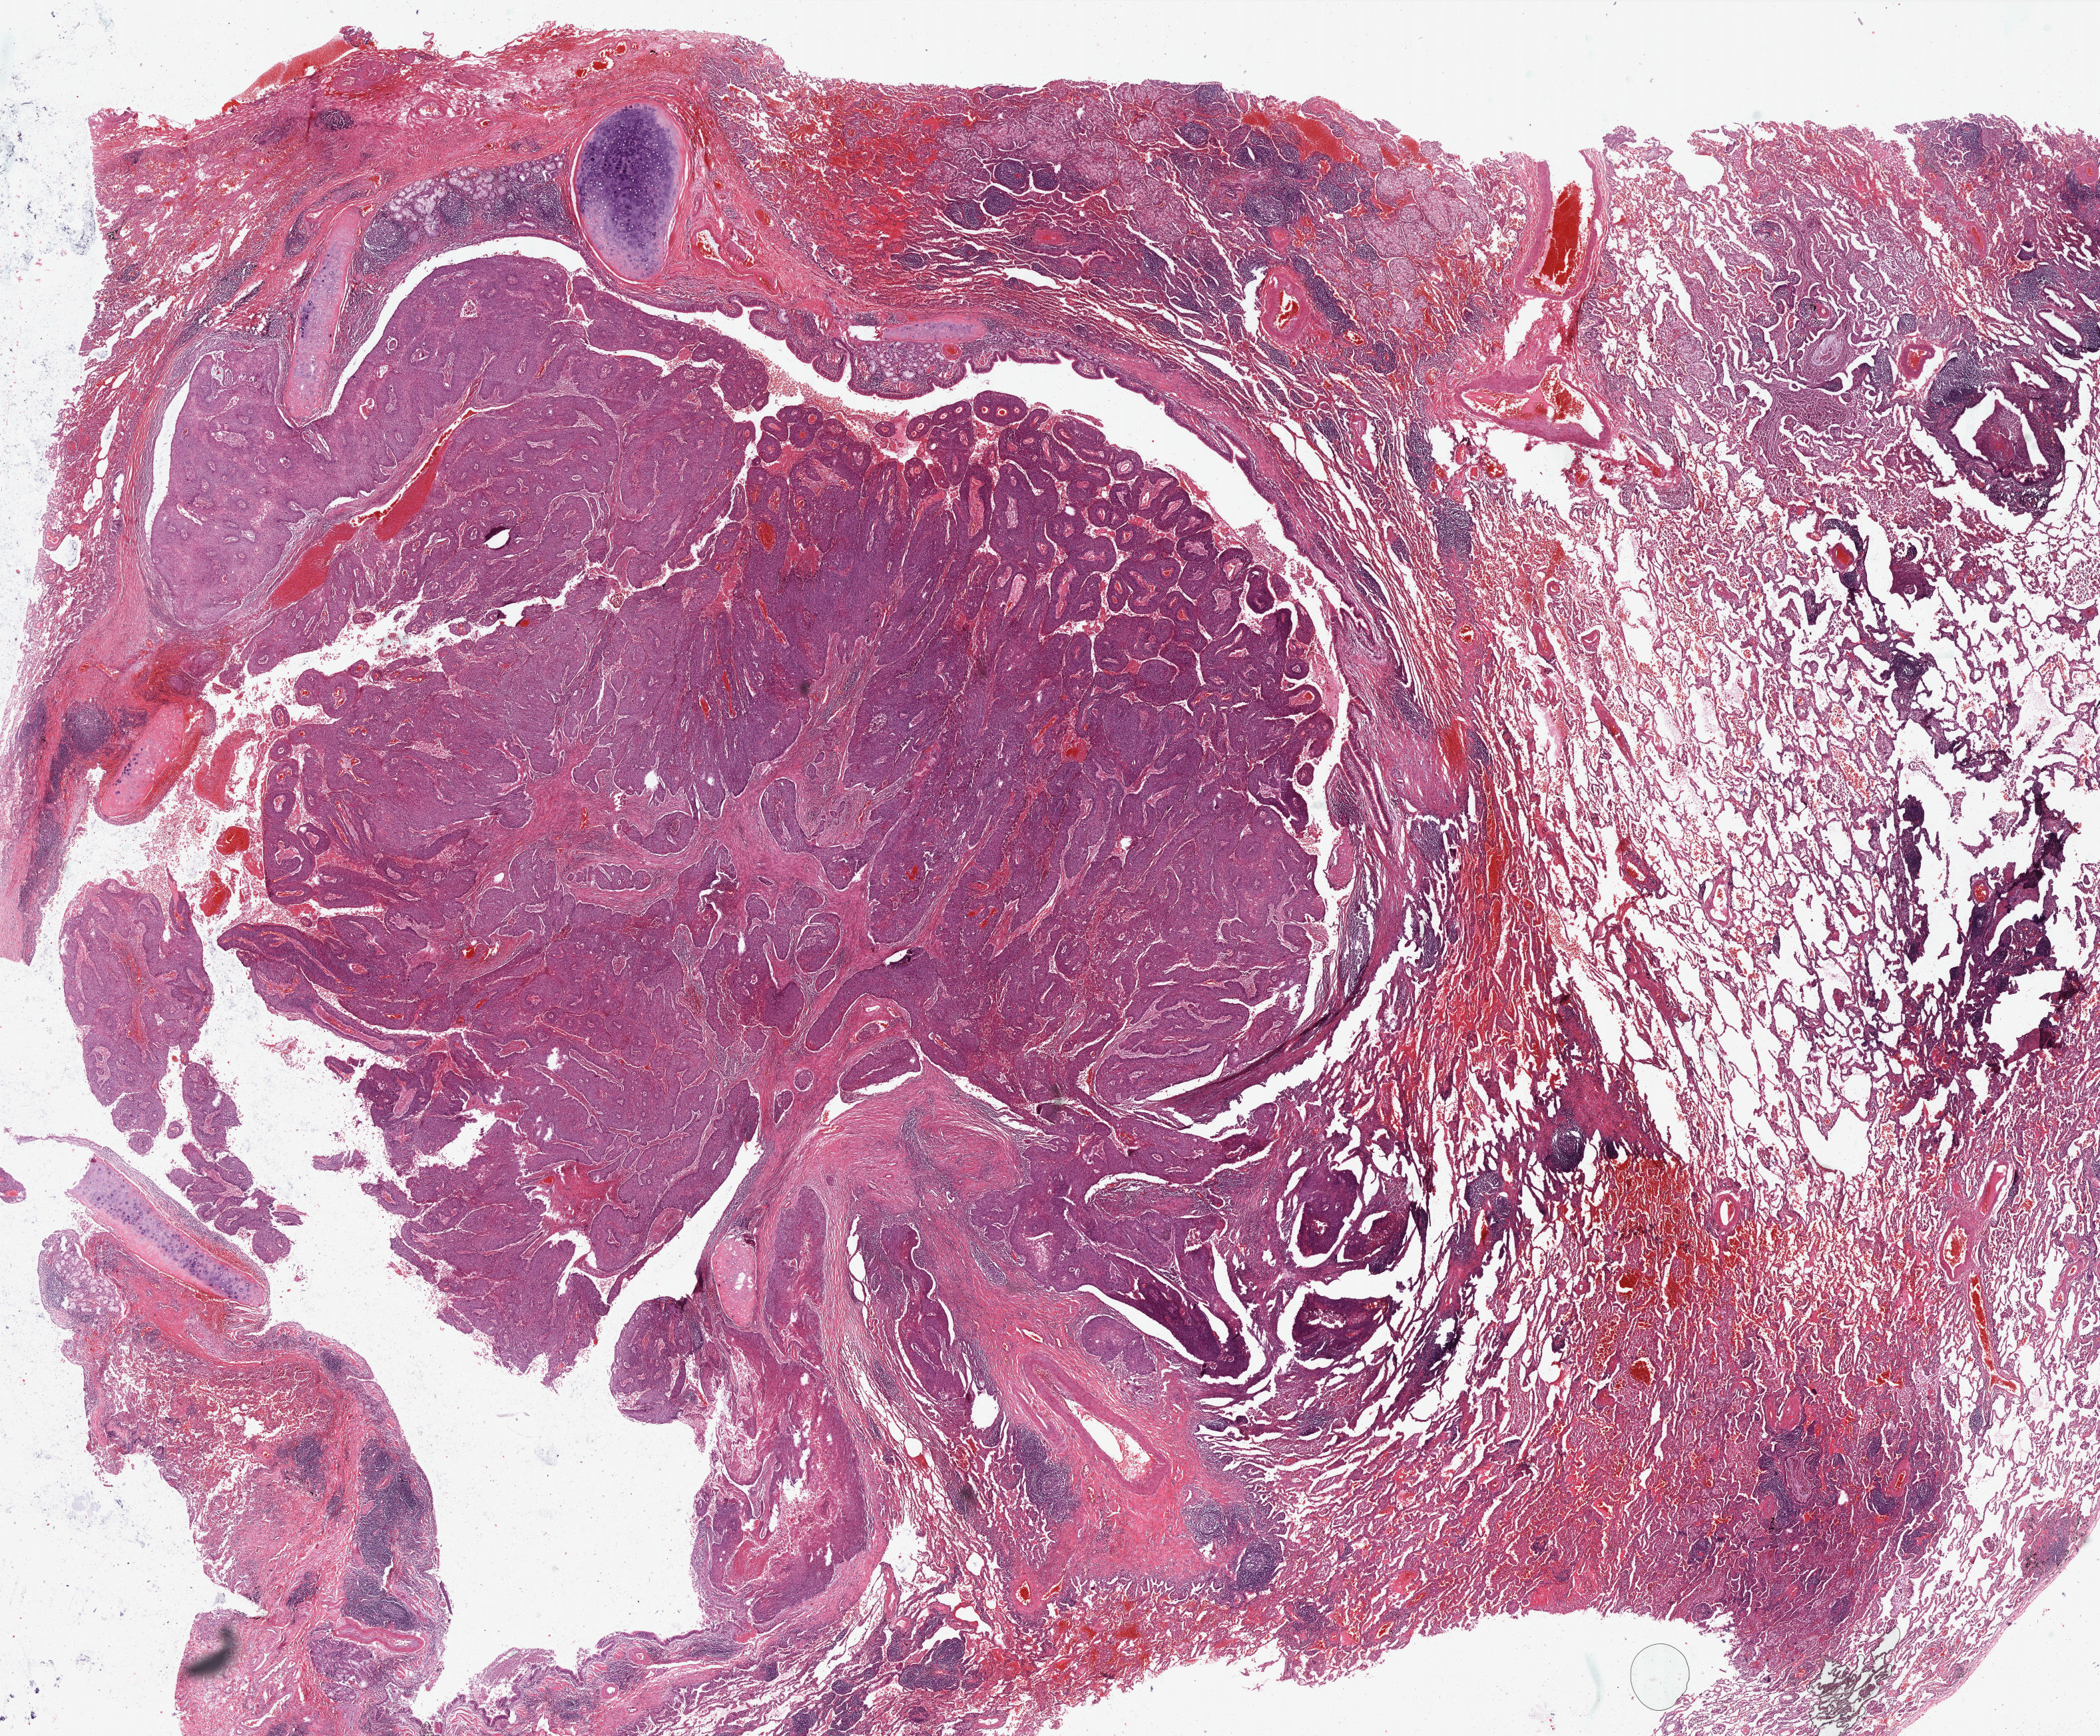
H&E whole-slide image — low-resolution overview of the scanned area, about 25.4 x 21.0 mm, formalin-fixed paraffin-embedded (FFPE) diagnostic section, primary tumour sample from the lung. Patient: male, age at initial diagnosis 52 years.
AJCC pathologic stage: IB (7th edition). Pathologic diagnosis: Basaloid squamous cell carcinoma.